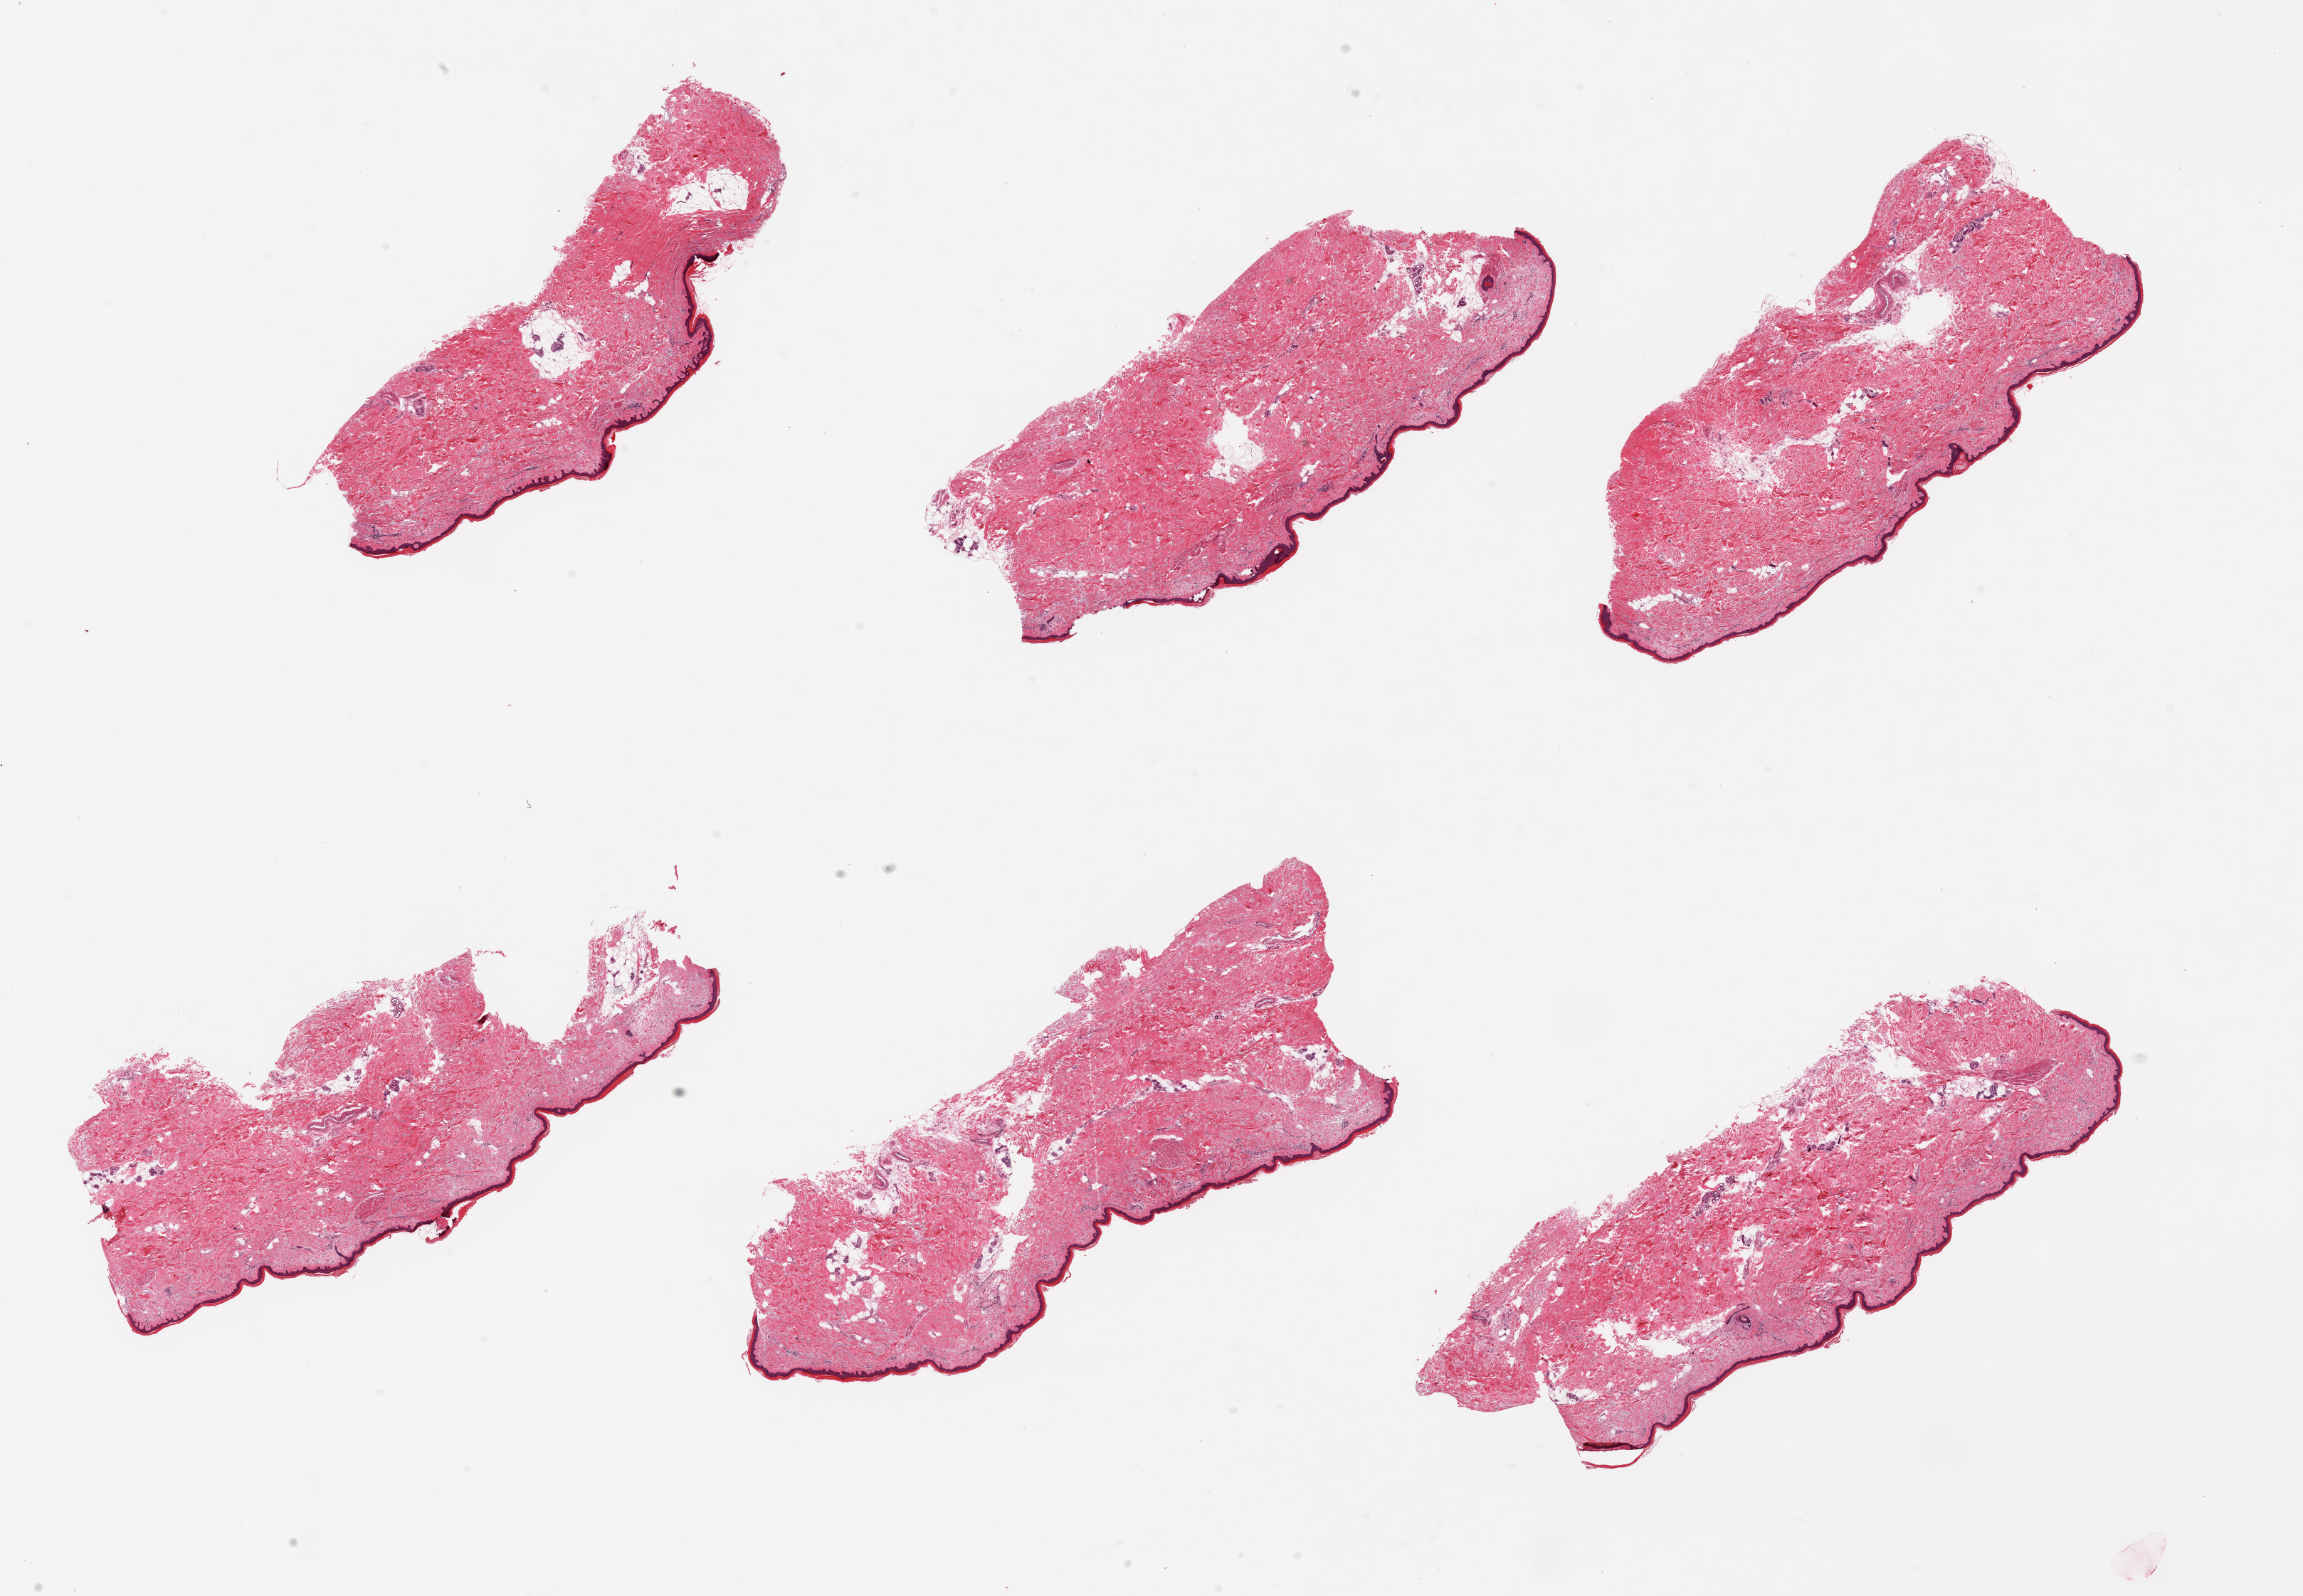
Digitized haematoxylin and eosin-stained section, brightfield, low-resolution overview of the scanned area, about 25.6 x 17.7 mm, PAXgene-fixed, paraffin-embedded tissue, target tissue: skin of lower leg, tissue donor sample.
Pathologist's review note for this sample: 6 pieces; well trimmed; 10% dermal fat.